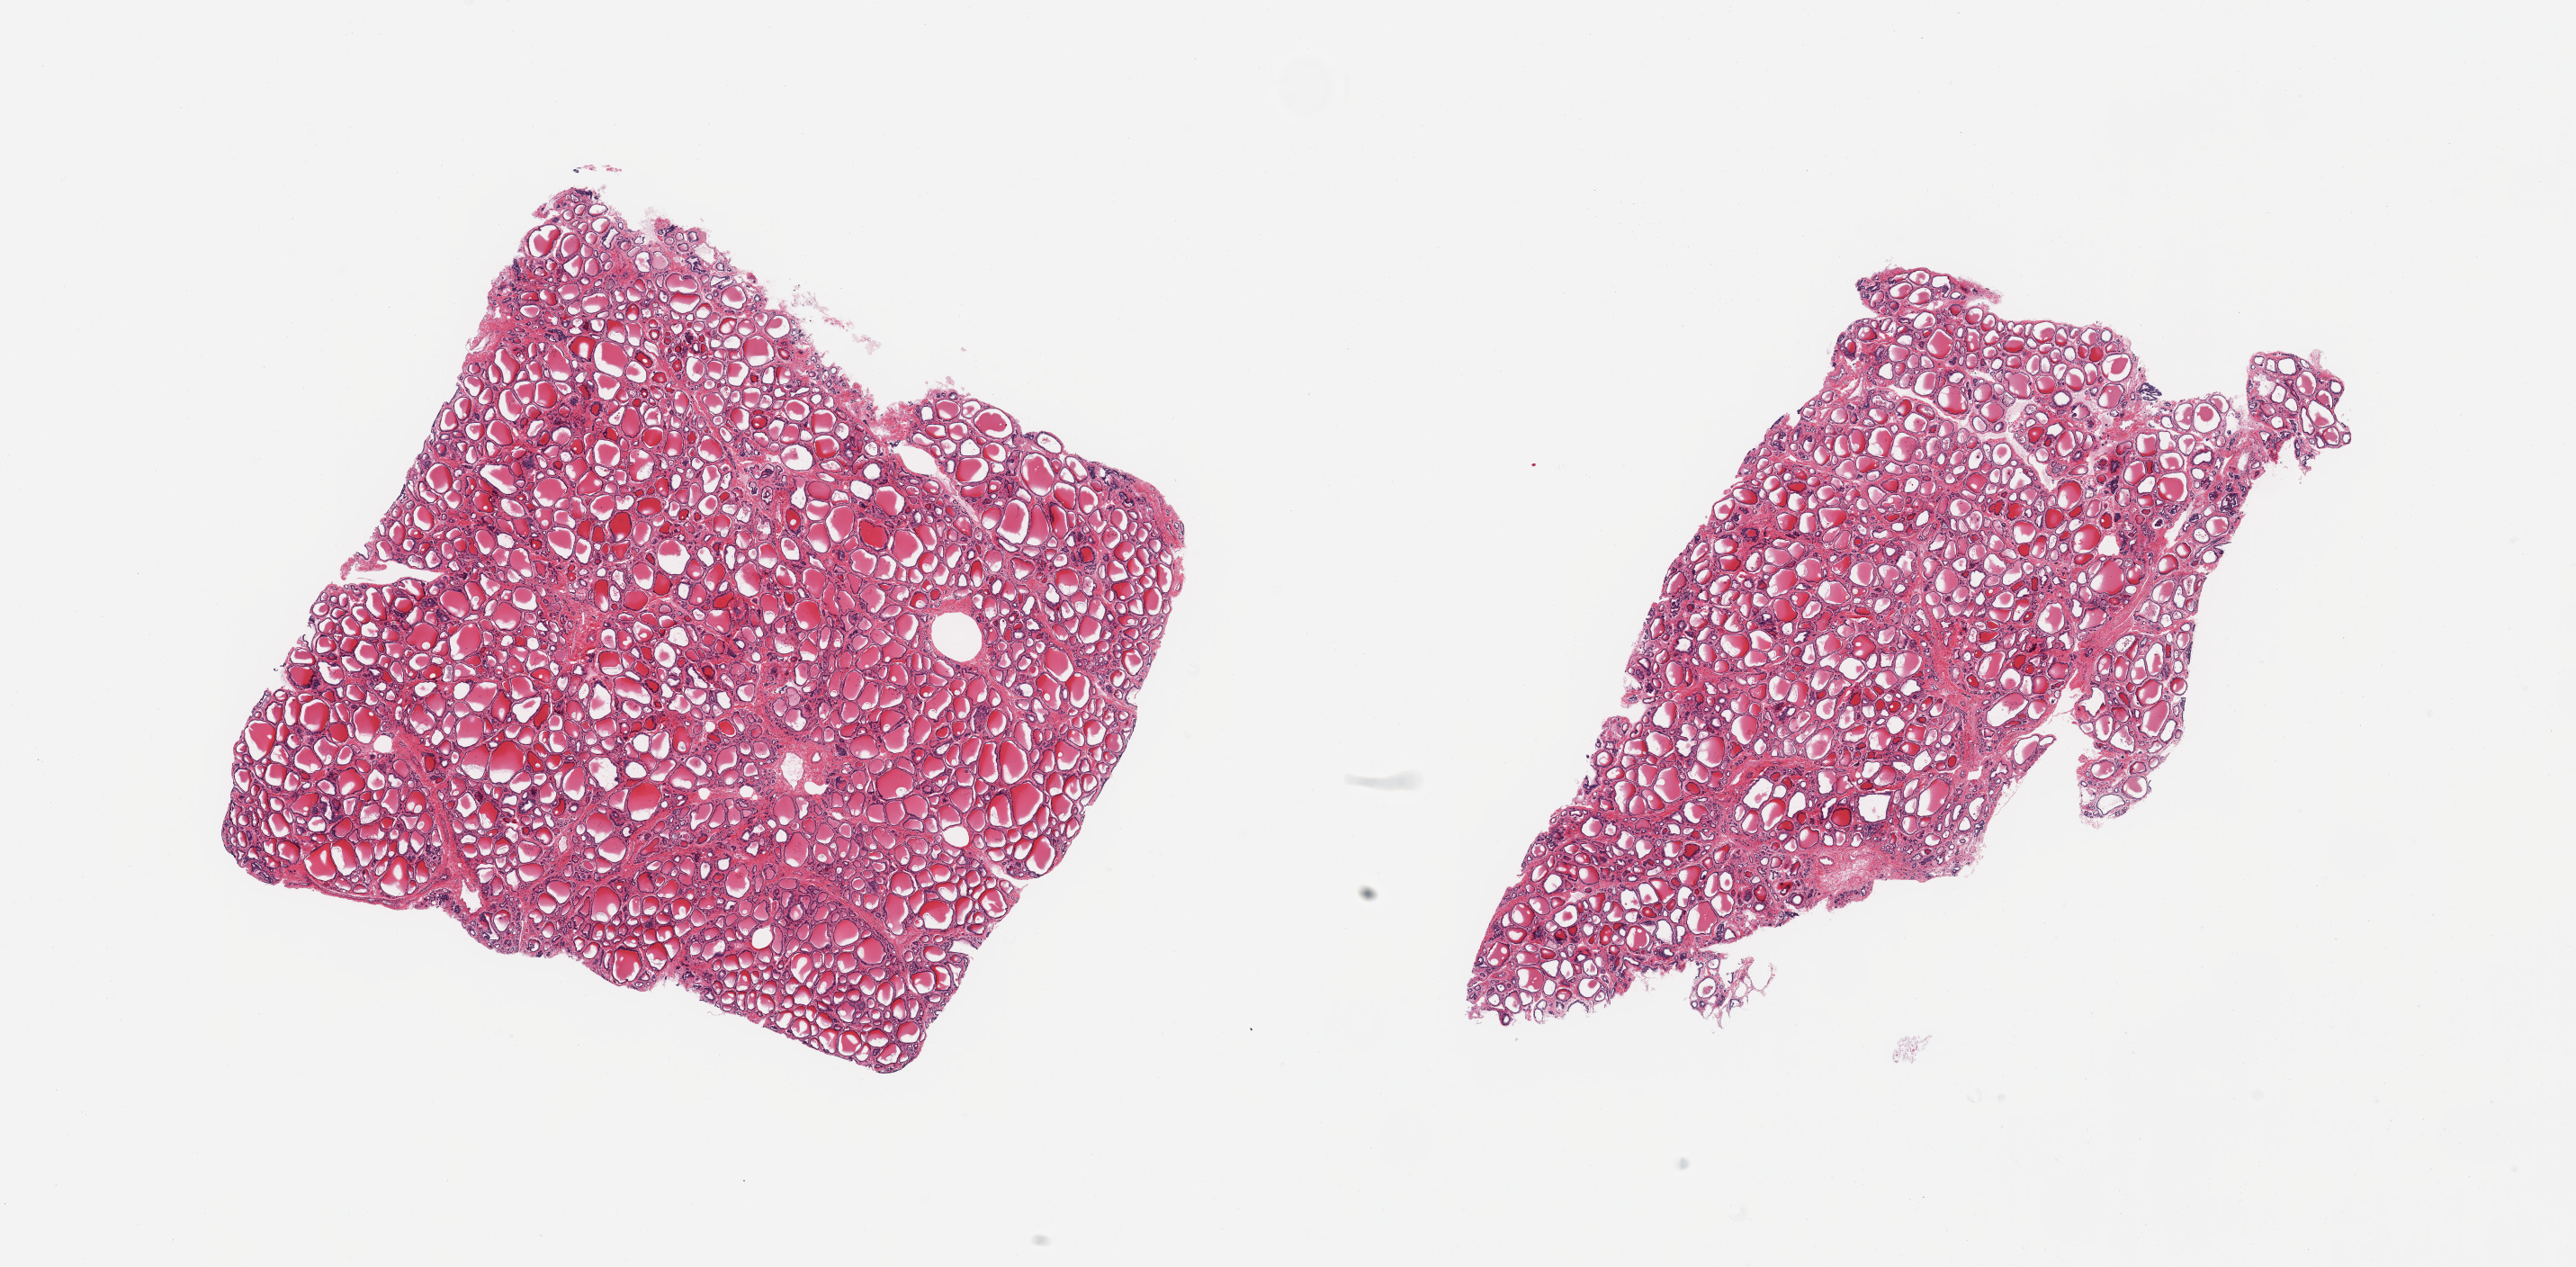
Digitized hematoxylin and eosin (H&E)-stained section, low-resolution overview of the scanned area, about 22.6 x 11.1 mm, PAXgene-fixed paraffin-embedded (PFPE) section, sampled site (target tissue): thyroid, donor tissue sample. Male donor.
Review note (as recorded): 2 pieces; no pathologic changes.